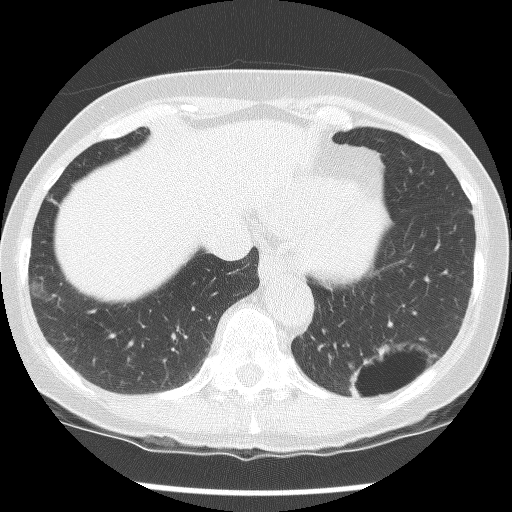
Chest CT (low-dose screening protocol), one axial image. Second annual screen. Lung window (W 1500 / L -600 HU). 2.5 mm slice thickness. Female participant, aged 61 years at enrolment.
Lesion marked by an expert reader, bounding box [x1, y1, x2, y2] px = [328, 315, 438, 413]. The screening reader recorded 2 non-calcified nodules or masses ≥4 mm on this exam (left lower lobe, left lower lobe); which of them this box marks is not recorded. Participant outcome: lung cancer diagnosed 585 days after this screen — non-small cell carcinoma, left lower lobe, poorly differentiated (G3), stage IB (AJCC 6th edition), 100 mm at pathology.